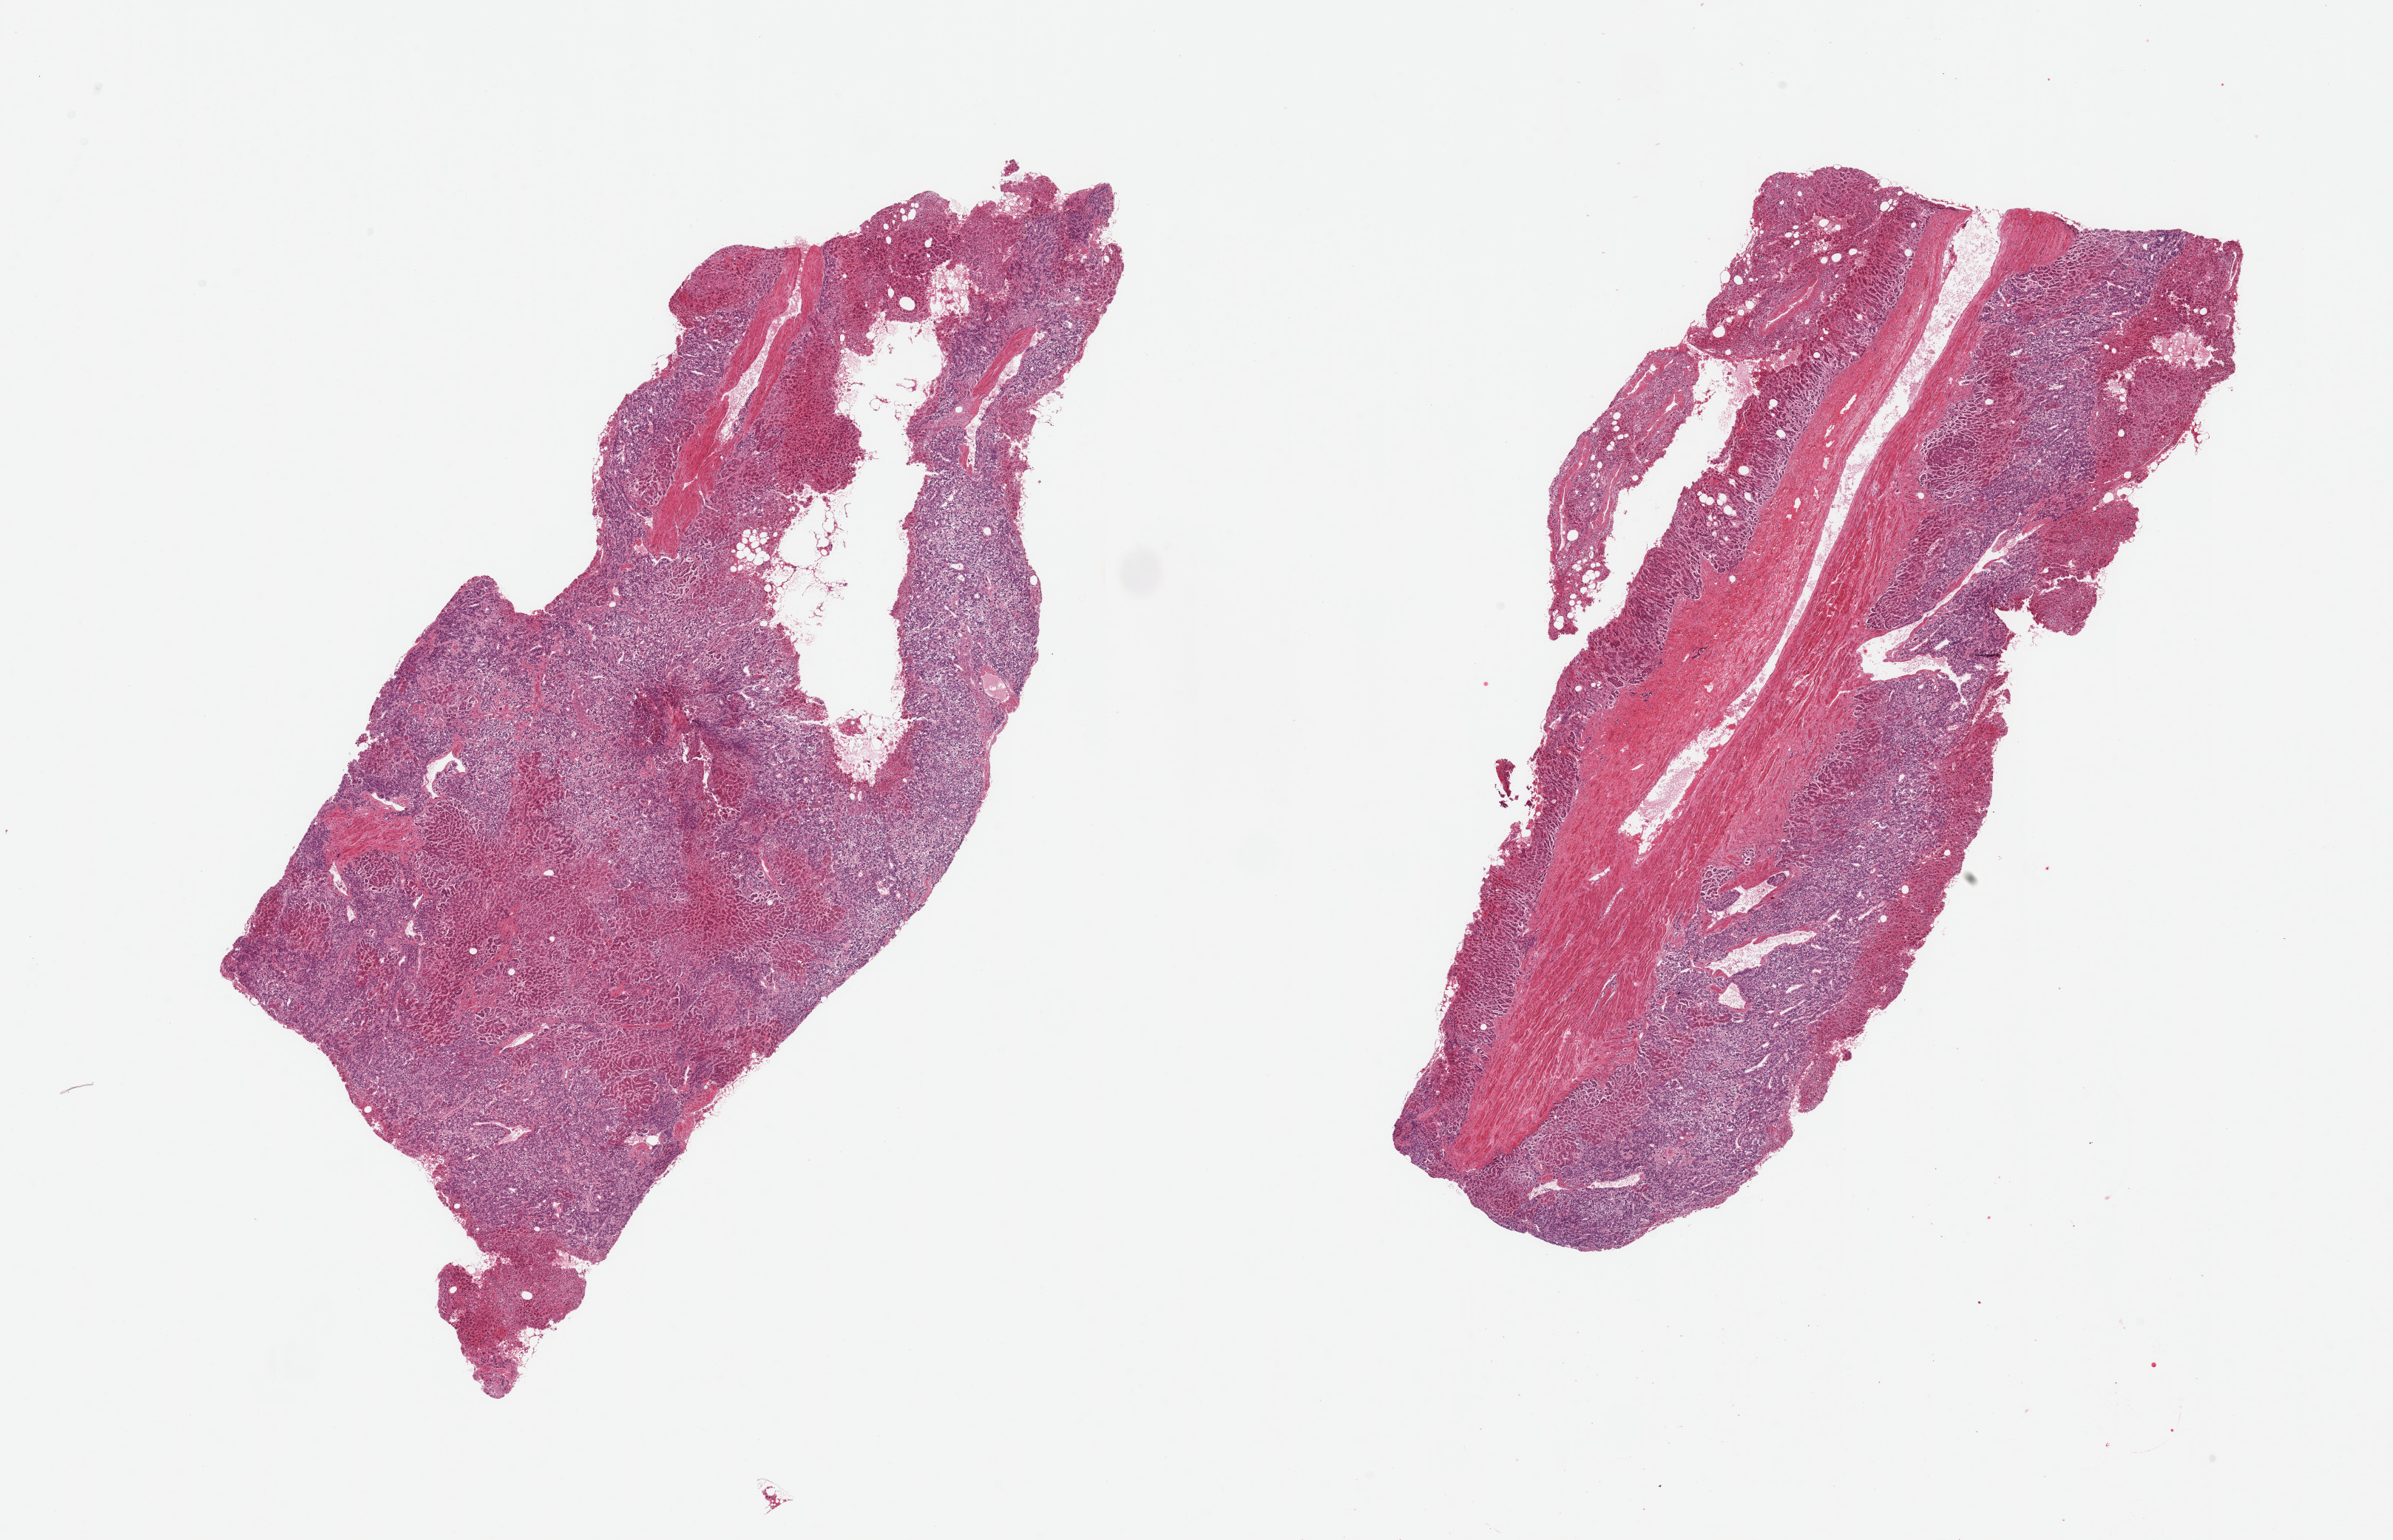
Haematoxylin and eosin whole-slide image, a low-resolution overview of the entire scanned area, about 25.6 x 16.5 mm (from a 20x scan). PAXgene-fixed paraffin-embedded (PFPE) section. Target tissue: adrenal gland. Donor tissue sample. Male donor.
* pathologist's review note for this sample: 2 pieces, cortex, 20% adherent smooth muscle/stroma/